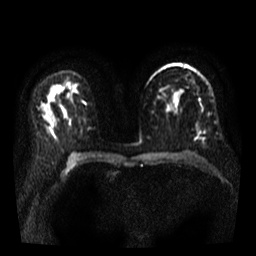
Breast MRI, one axial slice. Slice 22 of 35 in the series (ordered by position). Diffusion-weighted series; image 2 of 4 stored at this slice position (different b-values; order by instance number). 3 T. 256 × 256 image matrix, field of view 320 × 320 mm. Female patient.
Annotated regions visible in this slice (manually delineated by an expert):
- tumour on diffusion-weighted imaging: bounding box (x1, y1, x2, y2) in pixels: (196, 130, 201, 139)